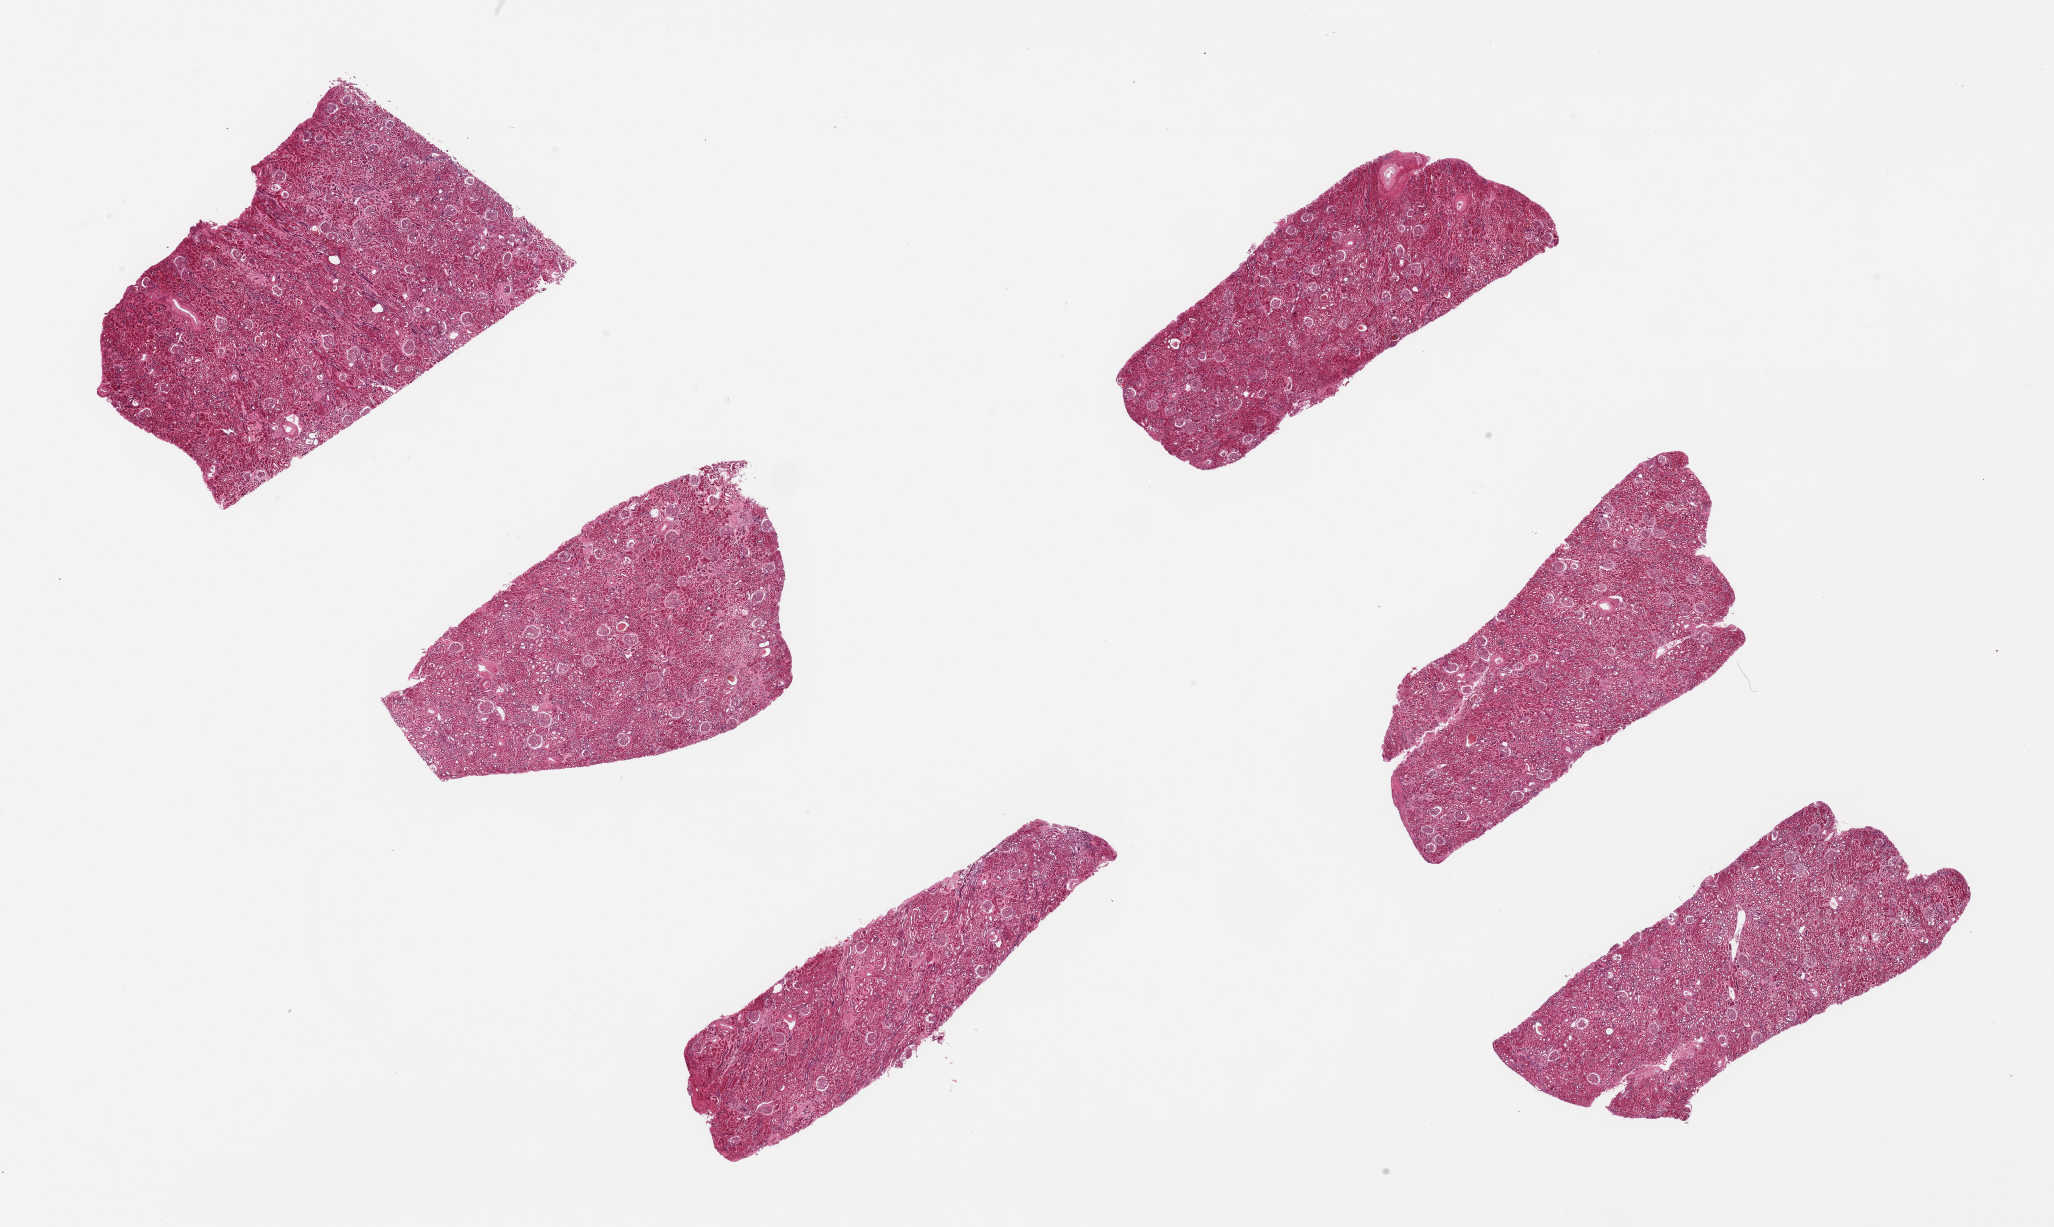
H&E whole-slide image, shown as a low-resolution overview of the whole scanned area (about 32.5 x 19.4 mm), PAXgene-fixed, paraffin-embedded tissue, sampled site (target tissue): renal cortex, donor tissue sample. Donor sex: male.
Pathologist's review note for this sample: 6 ~ 6.5x2-3mm pieces, all with glomeruli.